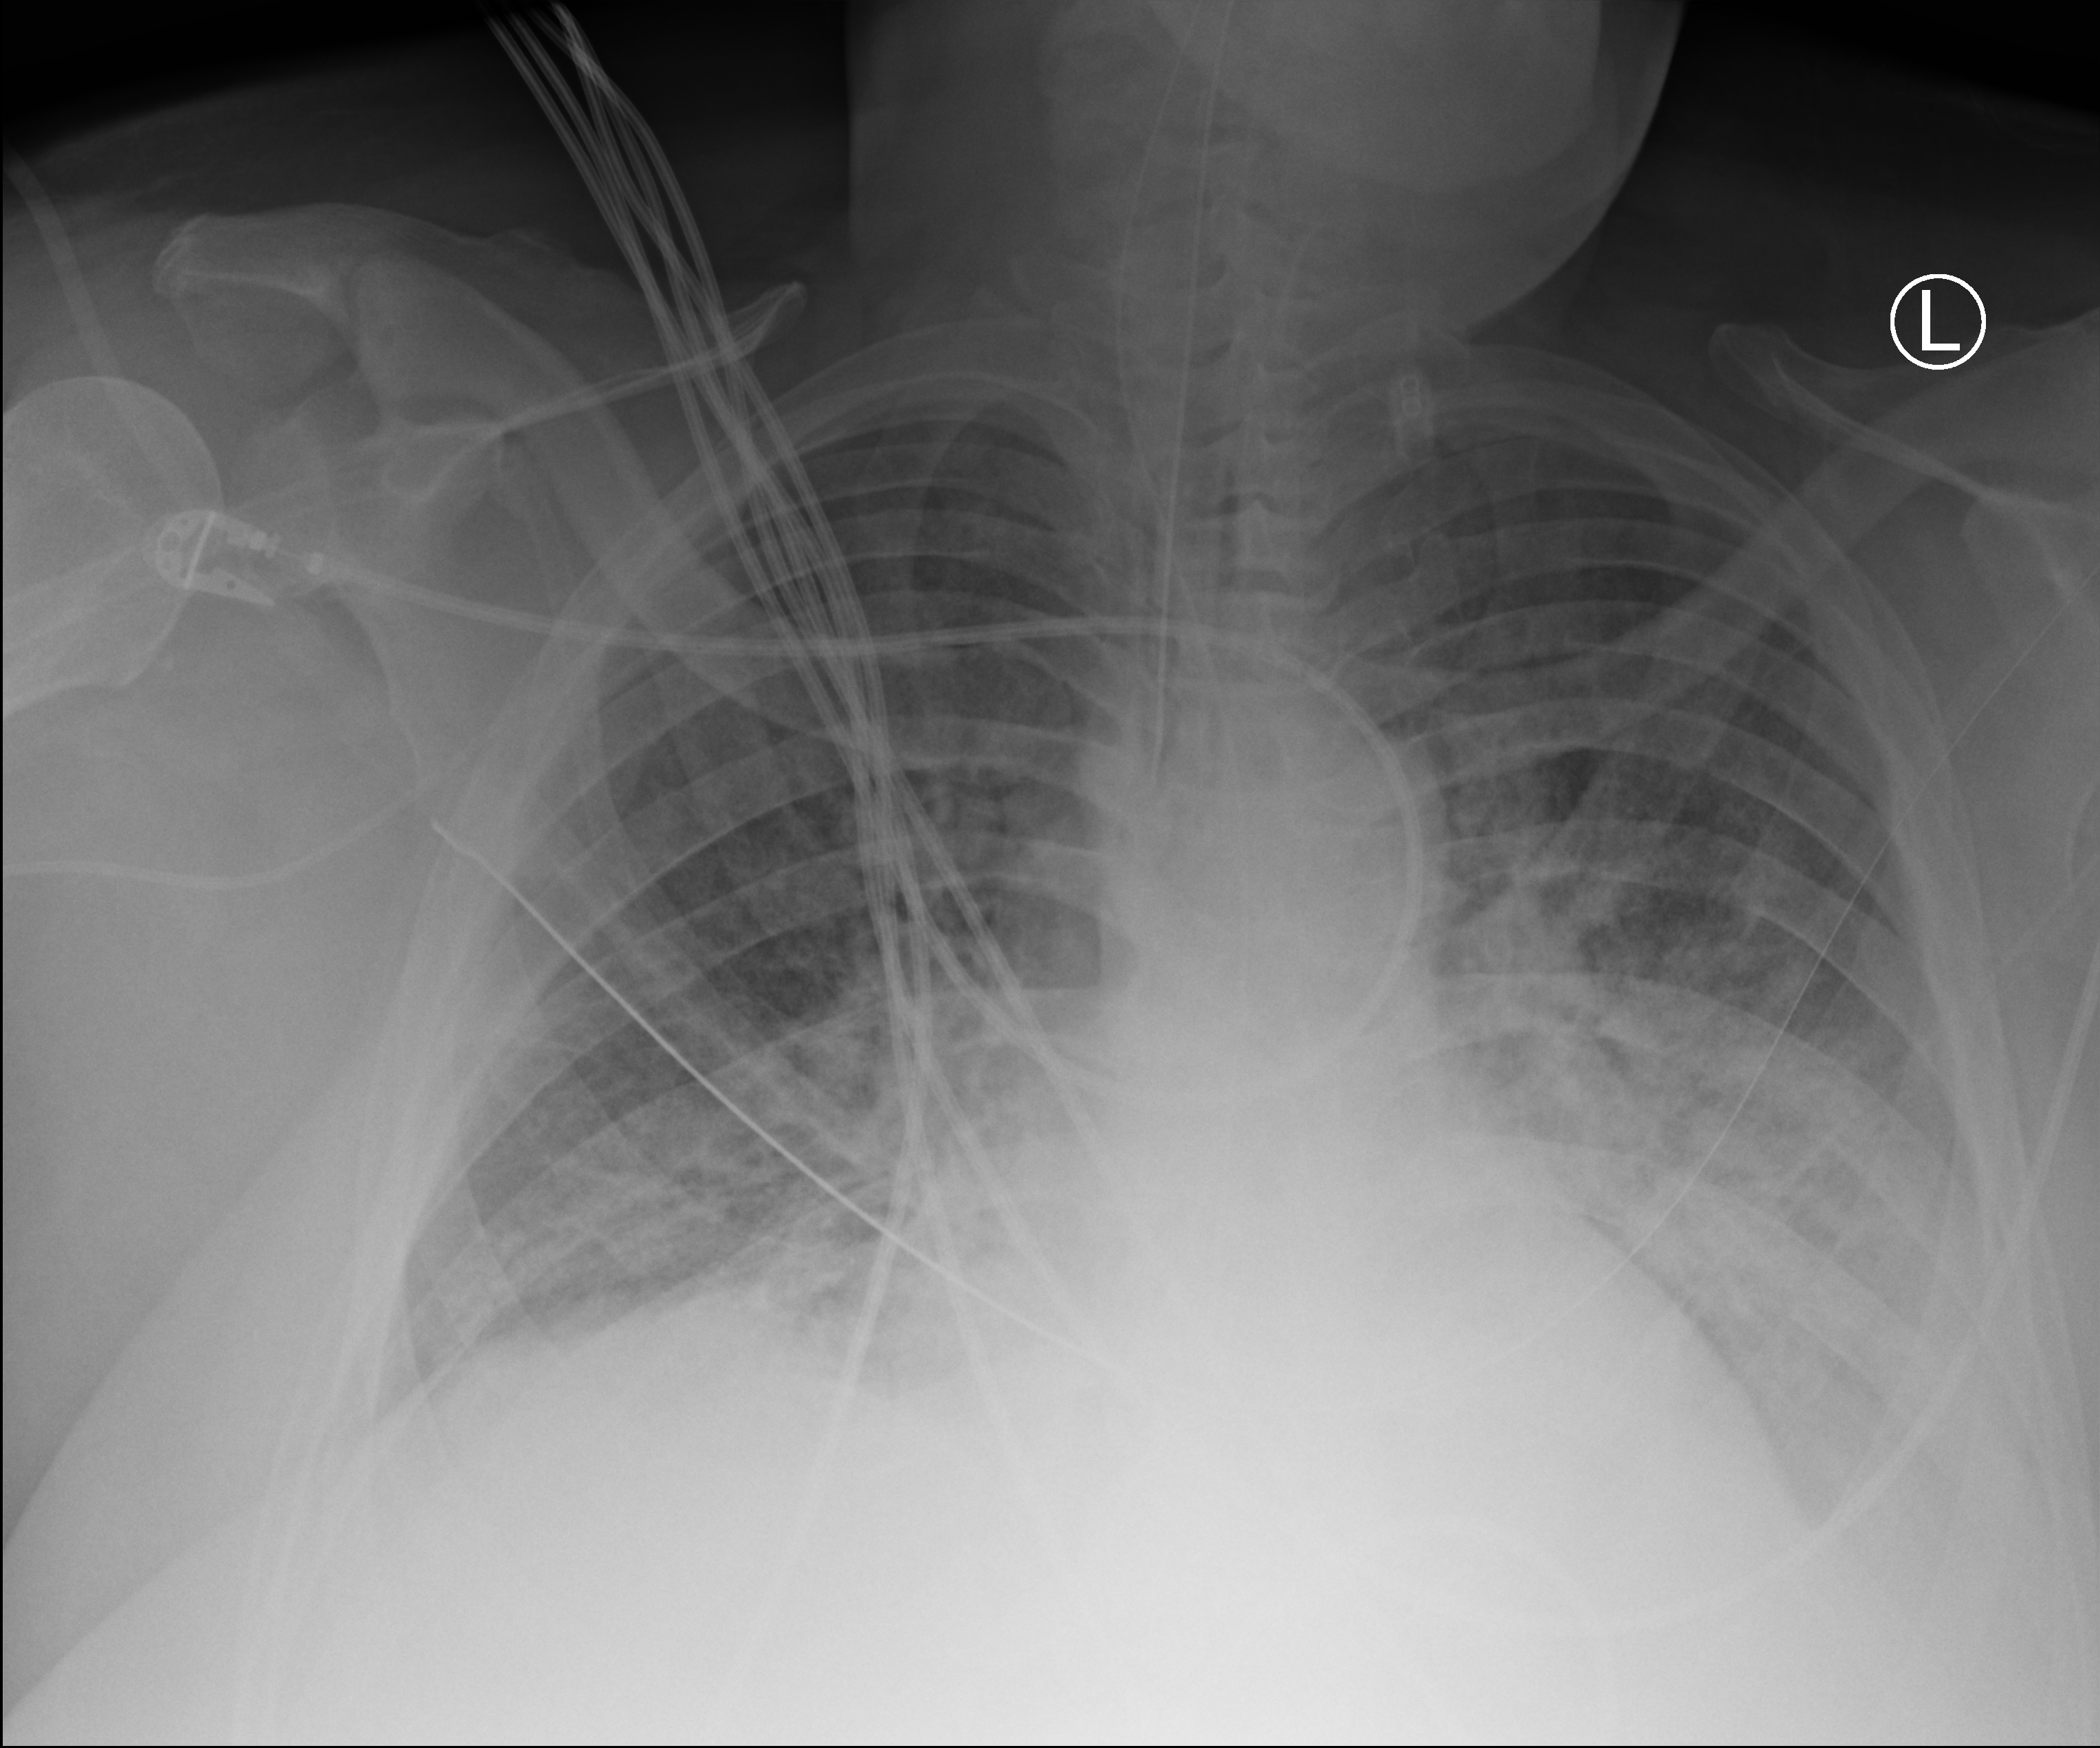
Chest X-ray (portable), anteroposterior (AP) projection. Male patient hospitalised with COVID-19, age 60–74 years.
Hospital-stay facts (about this admission, not read from this image; timing relative to this image not recorded): hypertension (admission record): yes.